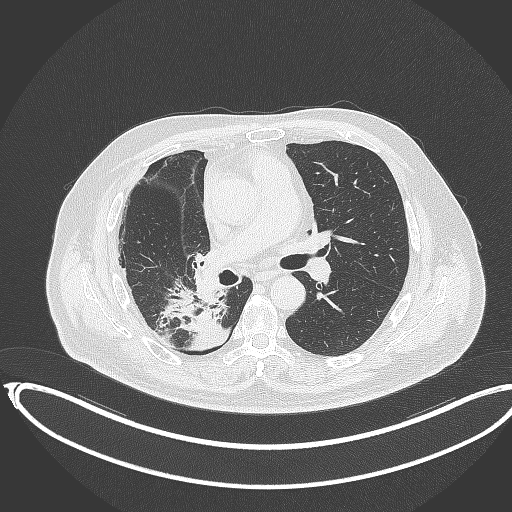
Chest CT, one axial slice; slice 196 of 403 in the series (ordered by position); reconstruction kernel B70f; 120 kVp; lung window (W 1500 / L -600 HU); 512 × 512 image matrix, field of view 436 × 436 mm. Male patient, age 68 years. Case-level facts recorded for this patient, not image findings: clinical TNM (as recorded): T2a N0 M0.
Structures marked on this image (rectangle marked by the reading radiologist):
- lung tumour (recorded histology: adenocarcinoma): bounding box (x1, y1, x2, y2) in pixels: (155, 294, 231, 353)